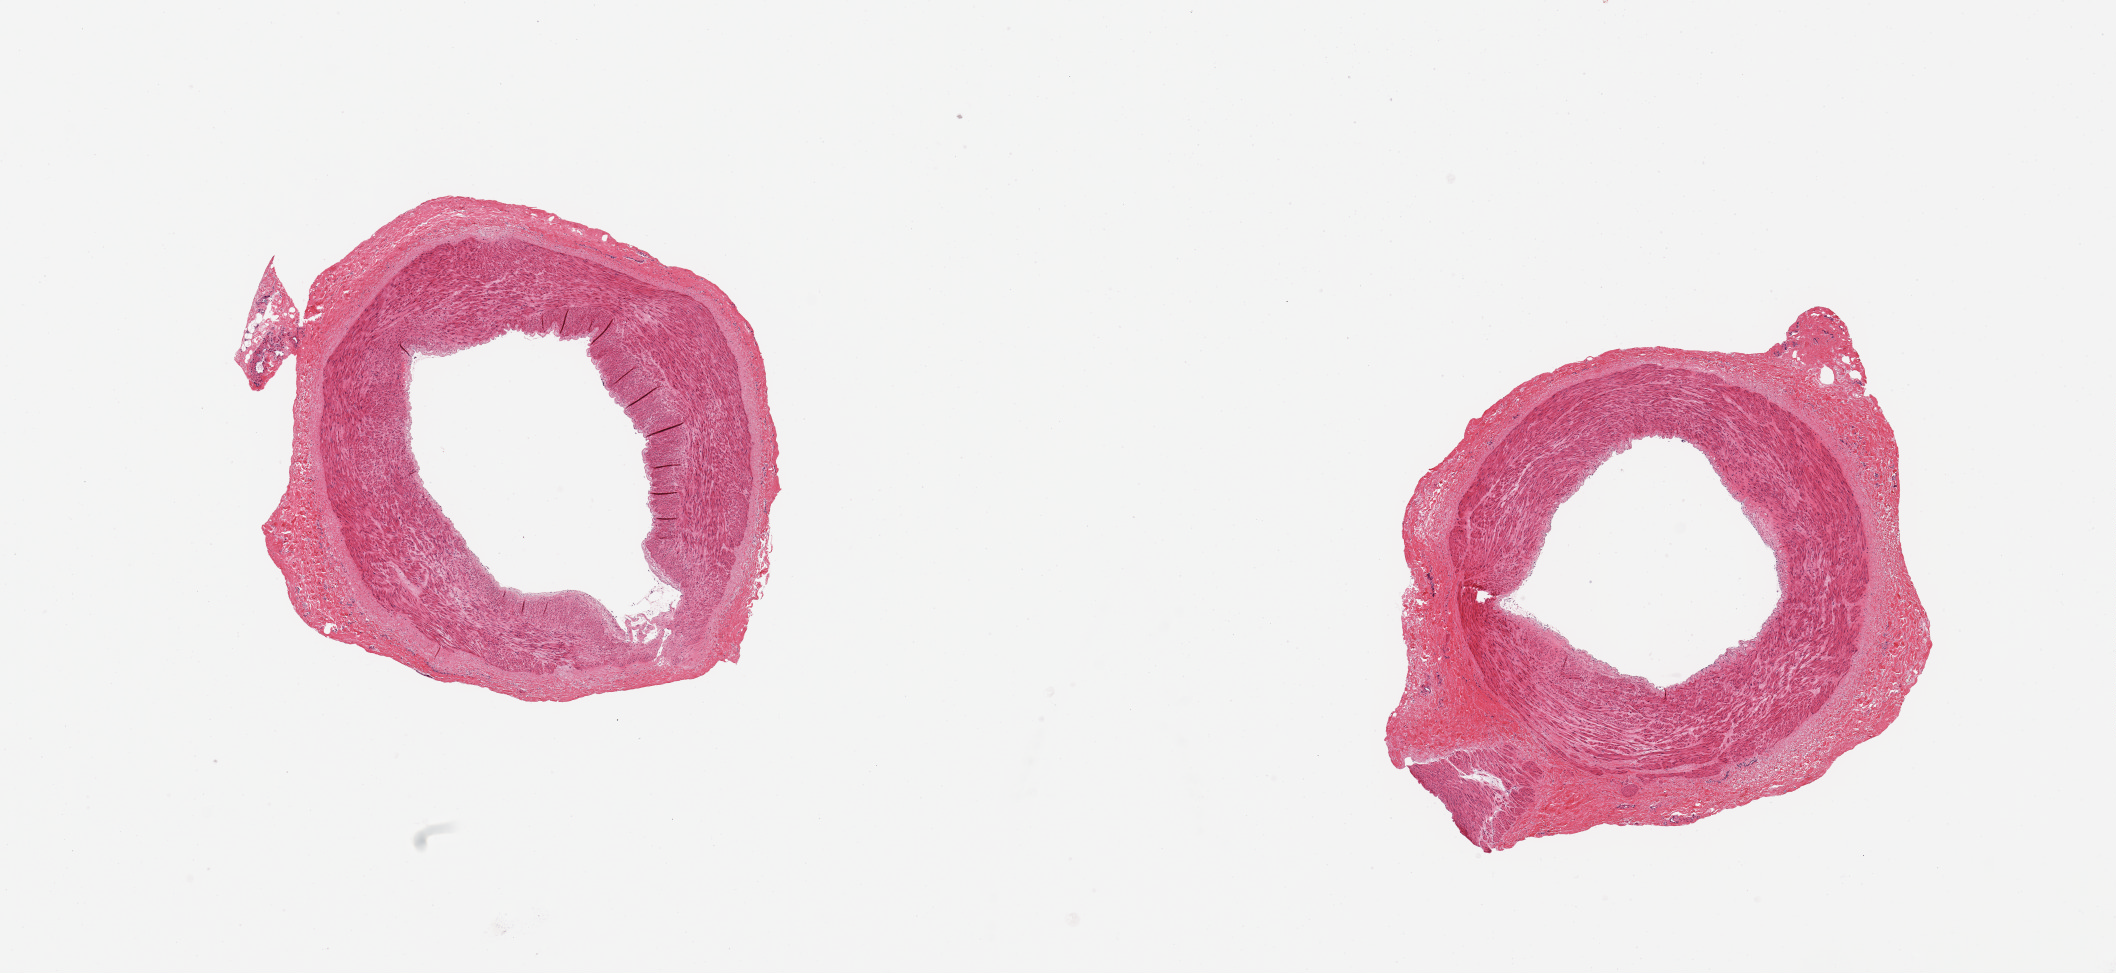
Hematoxylin and eosin (H&E) whole-slide image, low-resolution overview of the scanned area, about 16.7 x 7.7 mm (acquisition: 20x scan), PAXgene-fixed, paraffin-embedded tissue, target tissue: tibial artery, tissue donor sample. Donor: female.
Pathologist's review note for this sample: 2 pieces, clean specimens, minimal atherosis.